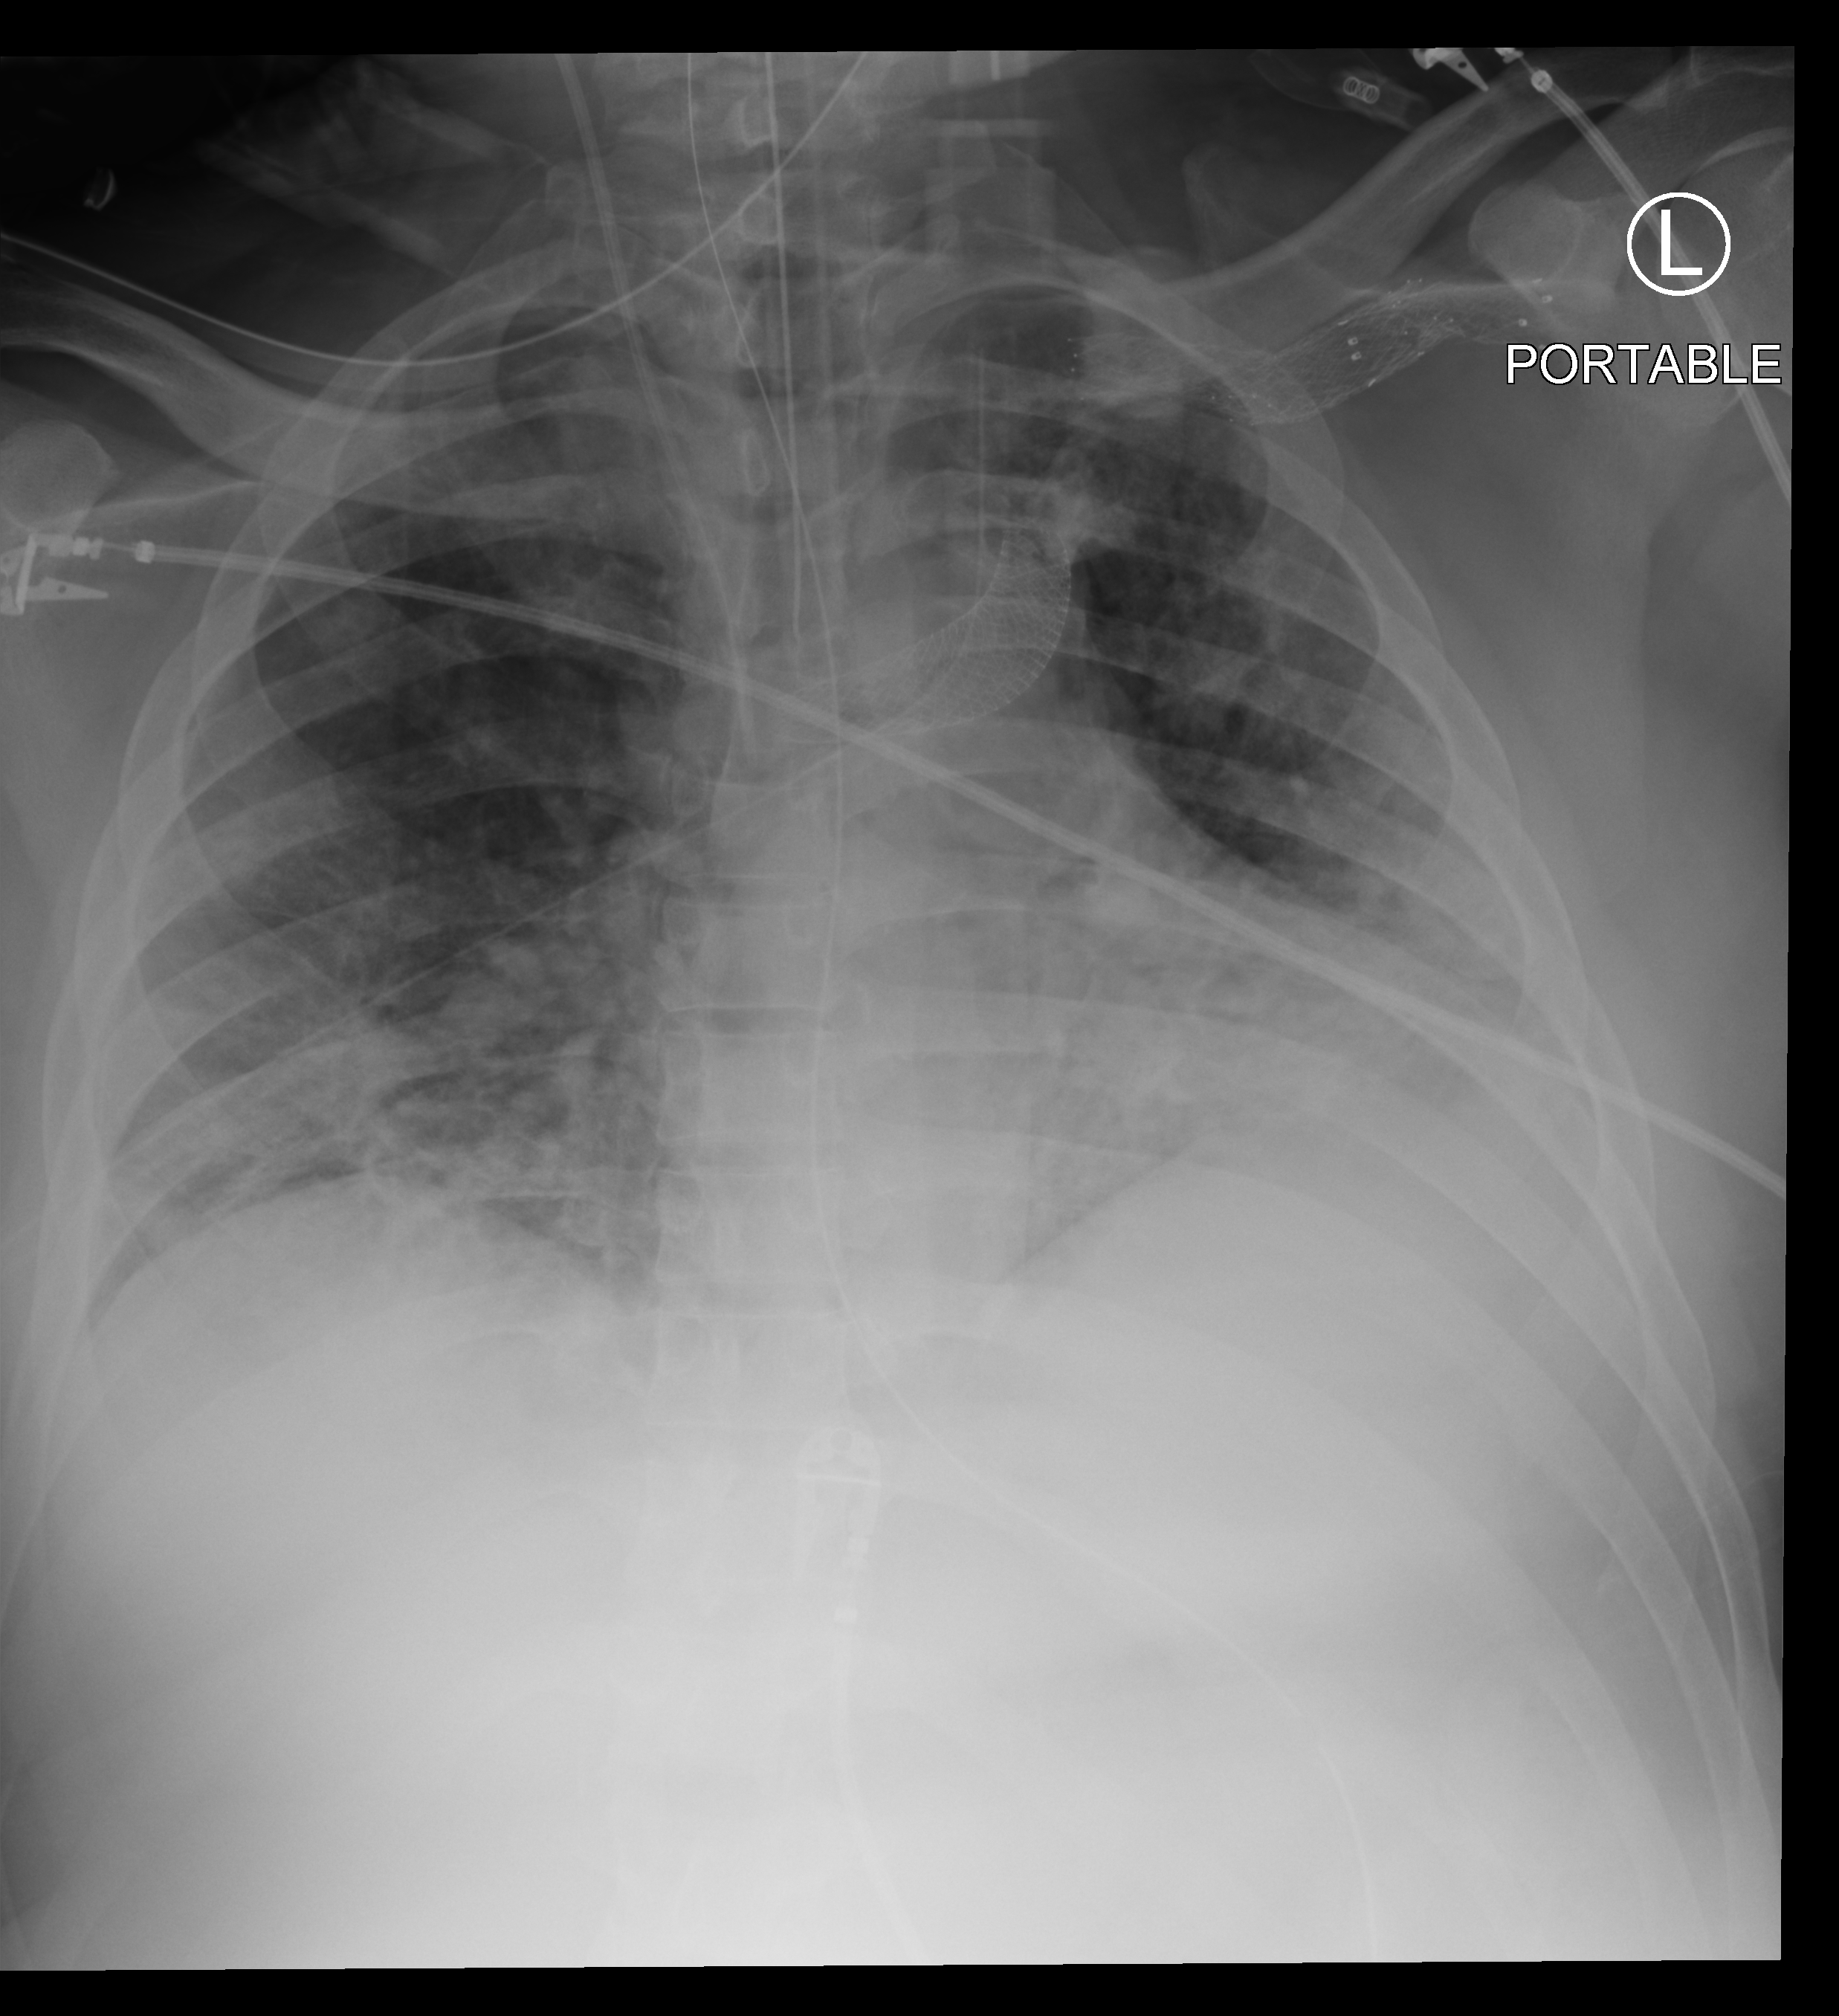
Portable chest radiograph; anteroposterior (AP) projection. Patient hospitalised with COVID-19; male, aged 18–59 years.
Hospital-stay facts (about this admission, not read from this image; timing relative to this image not recorded): mechanically ventilated during this hospital stay: yes.